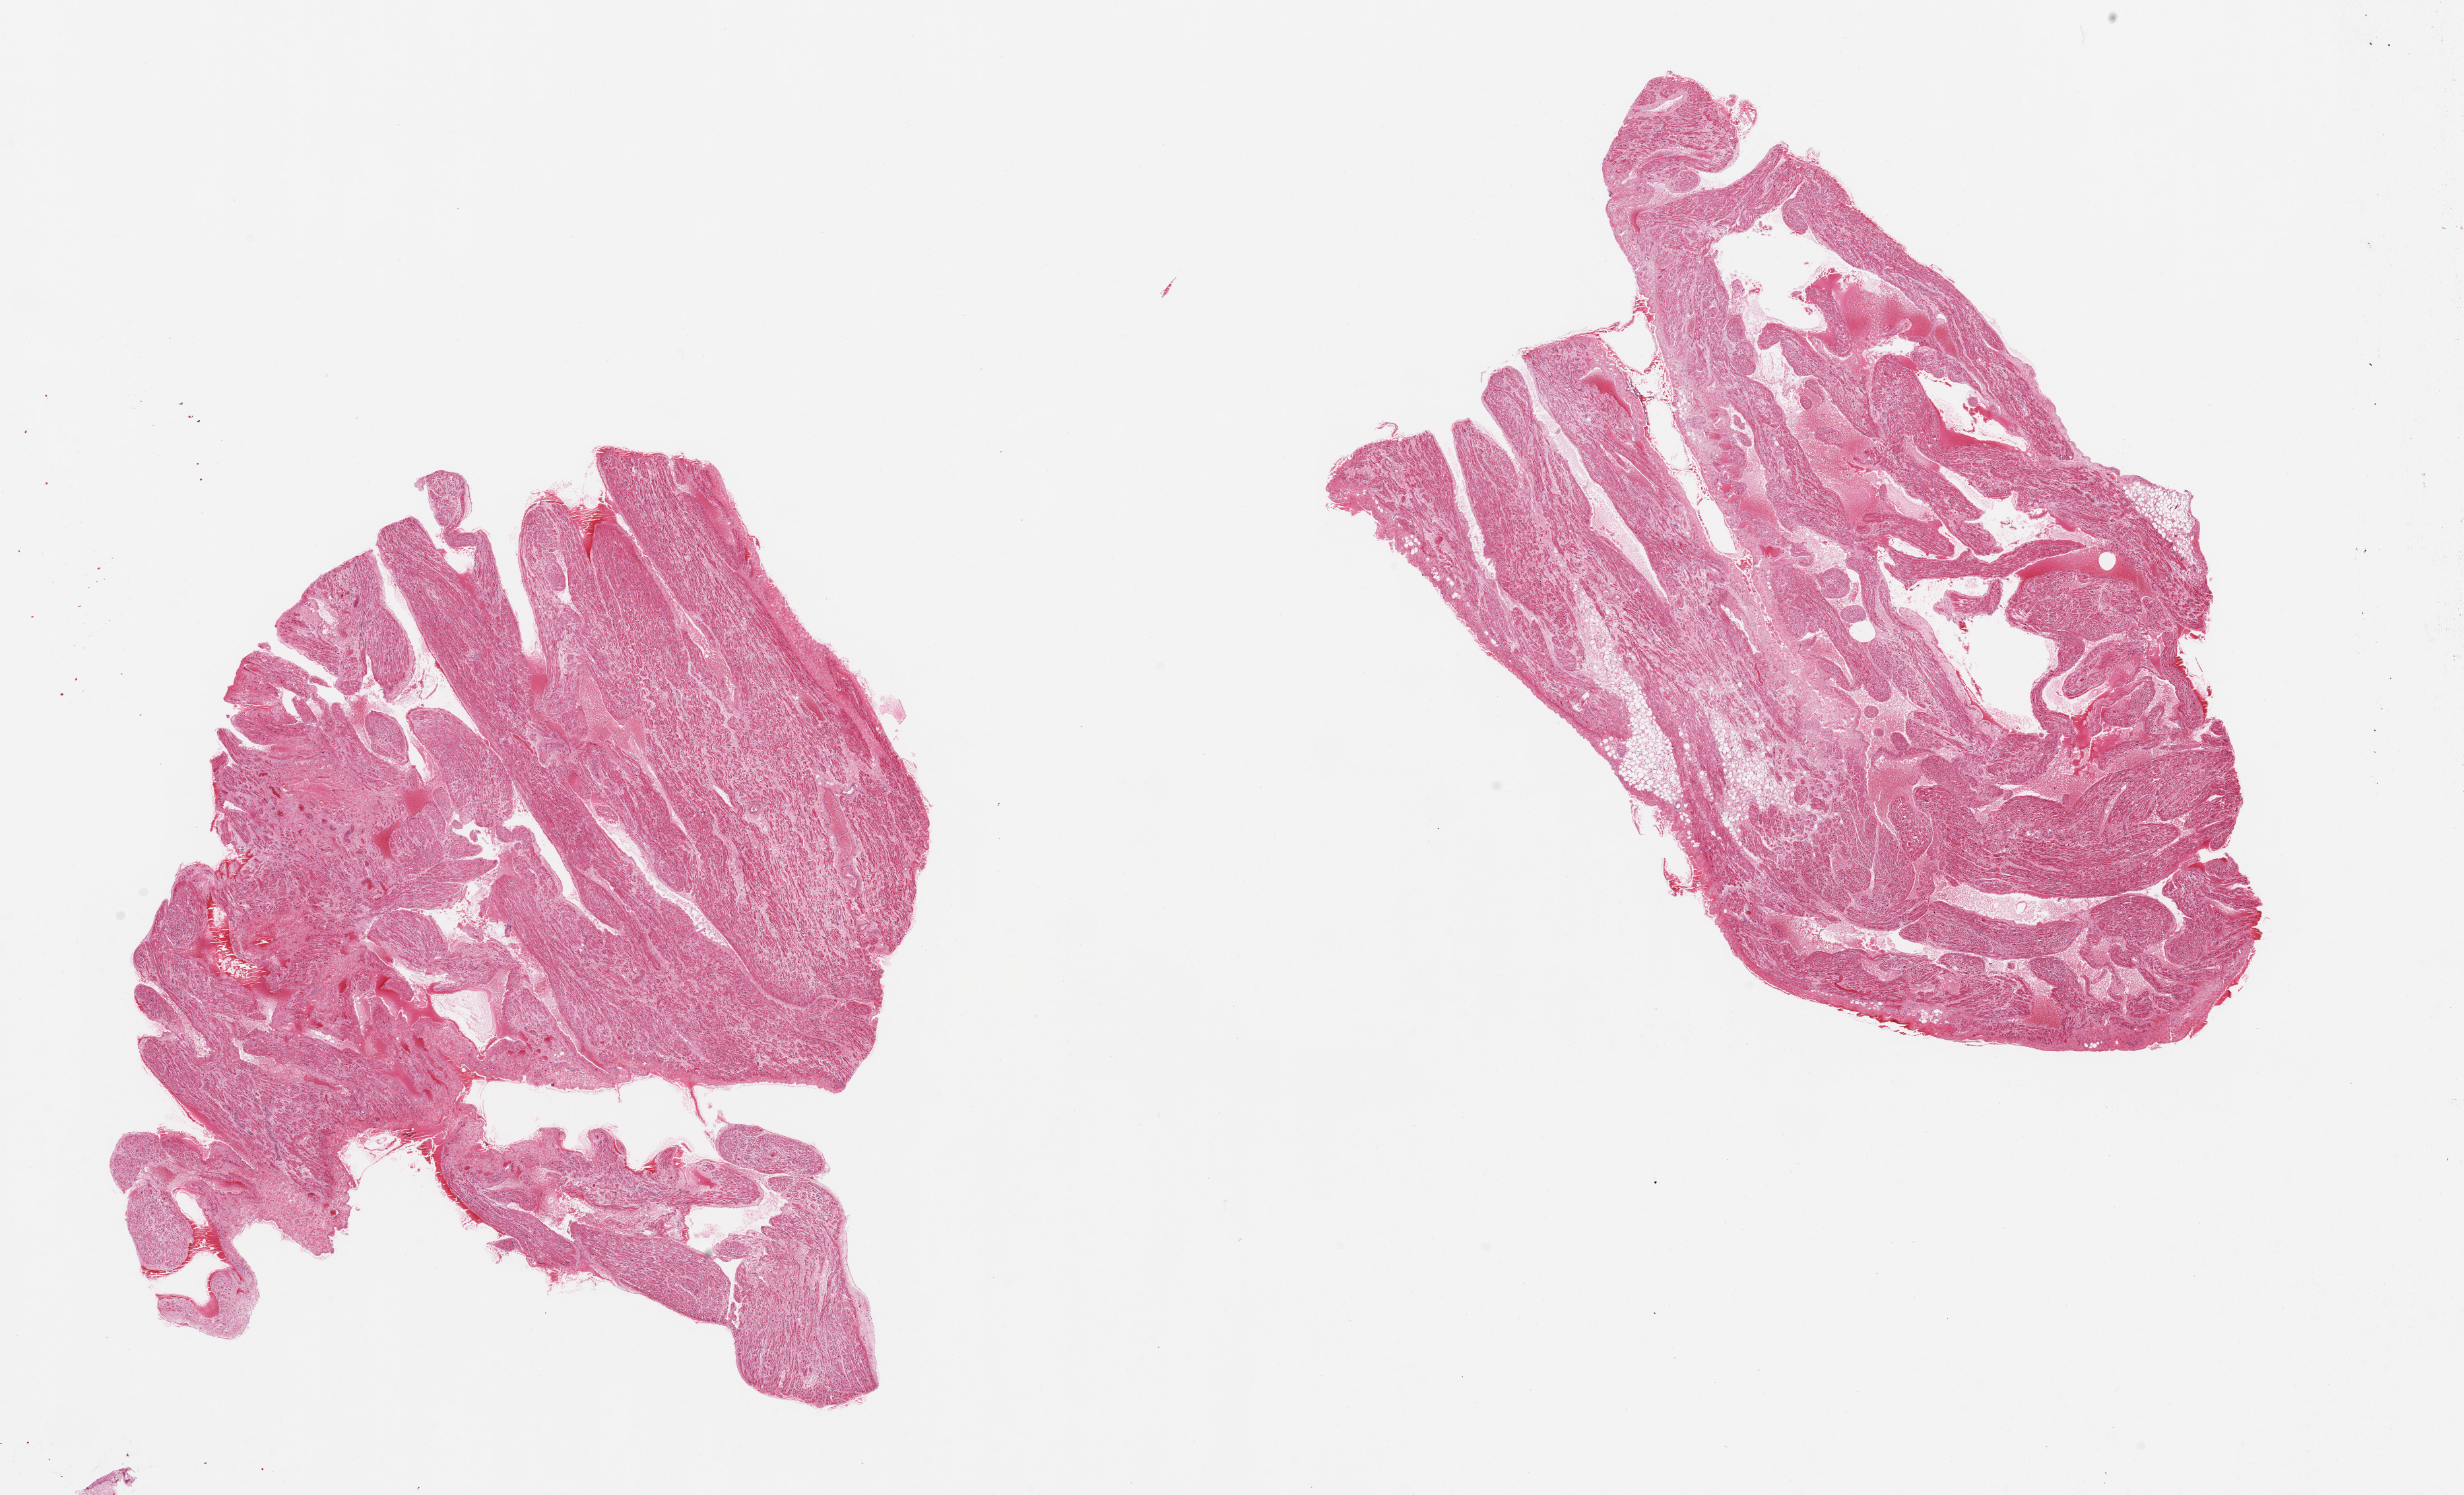
Whole-slide image, haematoxylin and eosin stain, brightfield — low-resolution overview of the scanned area, about 29.5 x 17.9 mm (slide scanned at 20x). PAXgene-fixed, paraffin-embedded tissue. Sampled site (target tissue): auricular appendage. Tissue donor sample.
* reviewer comment on this tissue sample: 2 pieces, no abnormalities